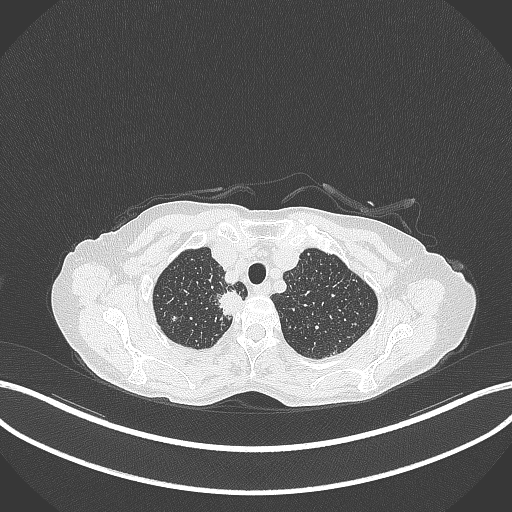
Chest CT, one axial slice; position 320 of 403 along the scan axis; reconstruction kernel B70f; lung window (W 1500 / L -600 HU); 1 mm slice thickness; 512 × 512 image matrix, field of view 400 × 400 mm. Female patient, age 75 years. Case-level facts recorded for this patient, not image findings: clinical TNM (as recorded): T1c N1 M1.
Structures marked on this image (bounding box drawn by a radiologist):
- lung tumour (recorded histology: adenocarcinoma): bounding box [x1, y1, x2, y2] px = [214, 288, 248, 321]